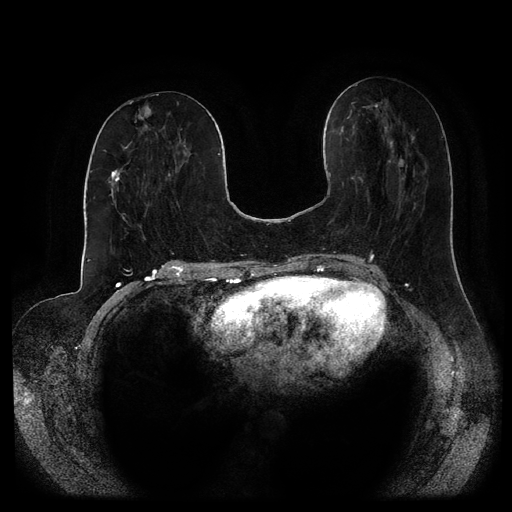
Breast MRI (dynamic contrast-enhanced, multi-phase), one axial slice; slice 43 of 116 in the series (ordered by position); dynamic contrast-enhanced series, time point 2 of 5 at this slice position (early post-contrast); 1.5 T; TE 2.6 ms, TR 5.2 ms; 512 × 512 image matrix. Female patient, age 53 years.
Structures marked on this image (semi-automatically segmented with operator editing):
- breast lesion (labelled 'tumour' in the annotation; benign lesions carry a separate 'benign' label): bounding box (x1, y1, x2, y2) in pixels: (134, 105, 152, 129)
- breast lesion (labelled 'tumour' in the annotation; benign lesions carry a separate 'benign' label): (111, 169, 121, 183)